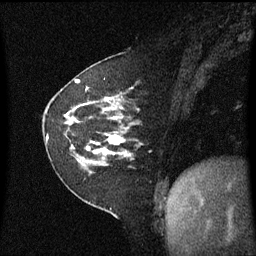
Breast MRI (dynamic contrast-enhanced), one sagittal slice; position 23 of 60 along the scan axis; dynamic contrast-enhanced series, image 2 of 3 at this slice position (ordered by acquisition); 1.5 T; TE 4.2 ms, TR 8.4 ms; 2 mm slice thickness; 256 × 256 image matrix, field of view 210 × 210 mm. Female patient, age 60 years. Case-level facts recorded for this patient, not image findings: setting: breast cancer imaged before/during neoadjuvant chemotherapy; receptor status: triple-negative.
Structures marked on this image (semi-automatic segmentation, software-assisted and operator-edited):
- analysis volume of interest (the breast-tissue region the enhancement analysis was run in; not a lesion): bounding box [x1, y1, x2, y2] px = [45, 99, 140, 182]
- tumour enhancement mask (voxels above the 70 % enhancement threshold inside the analysis volume of interest): [88, 99, 125, 156]